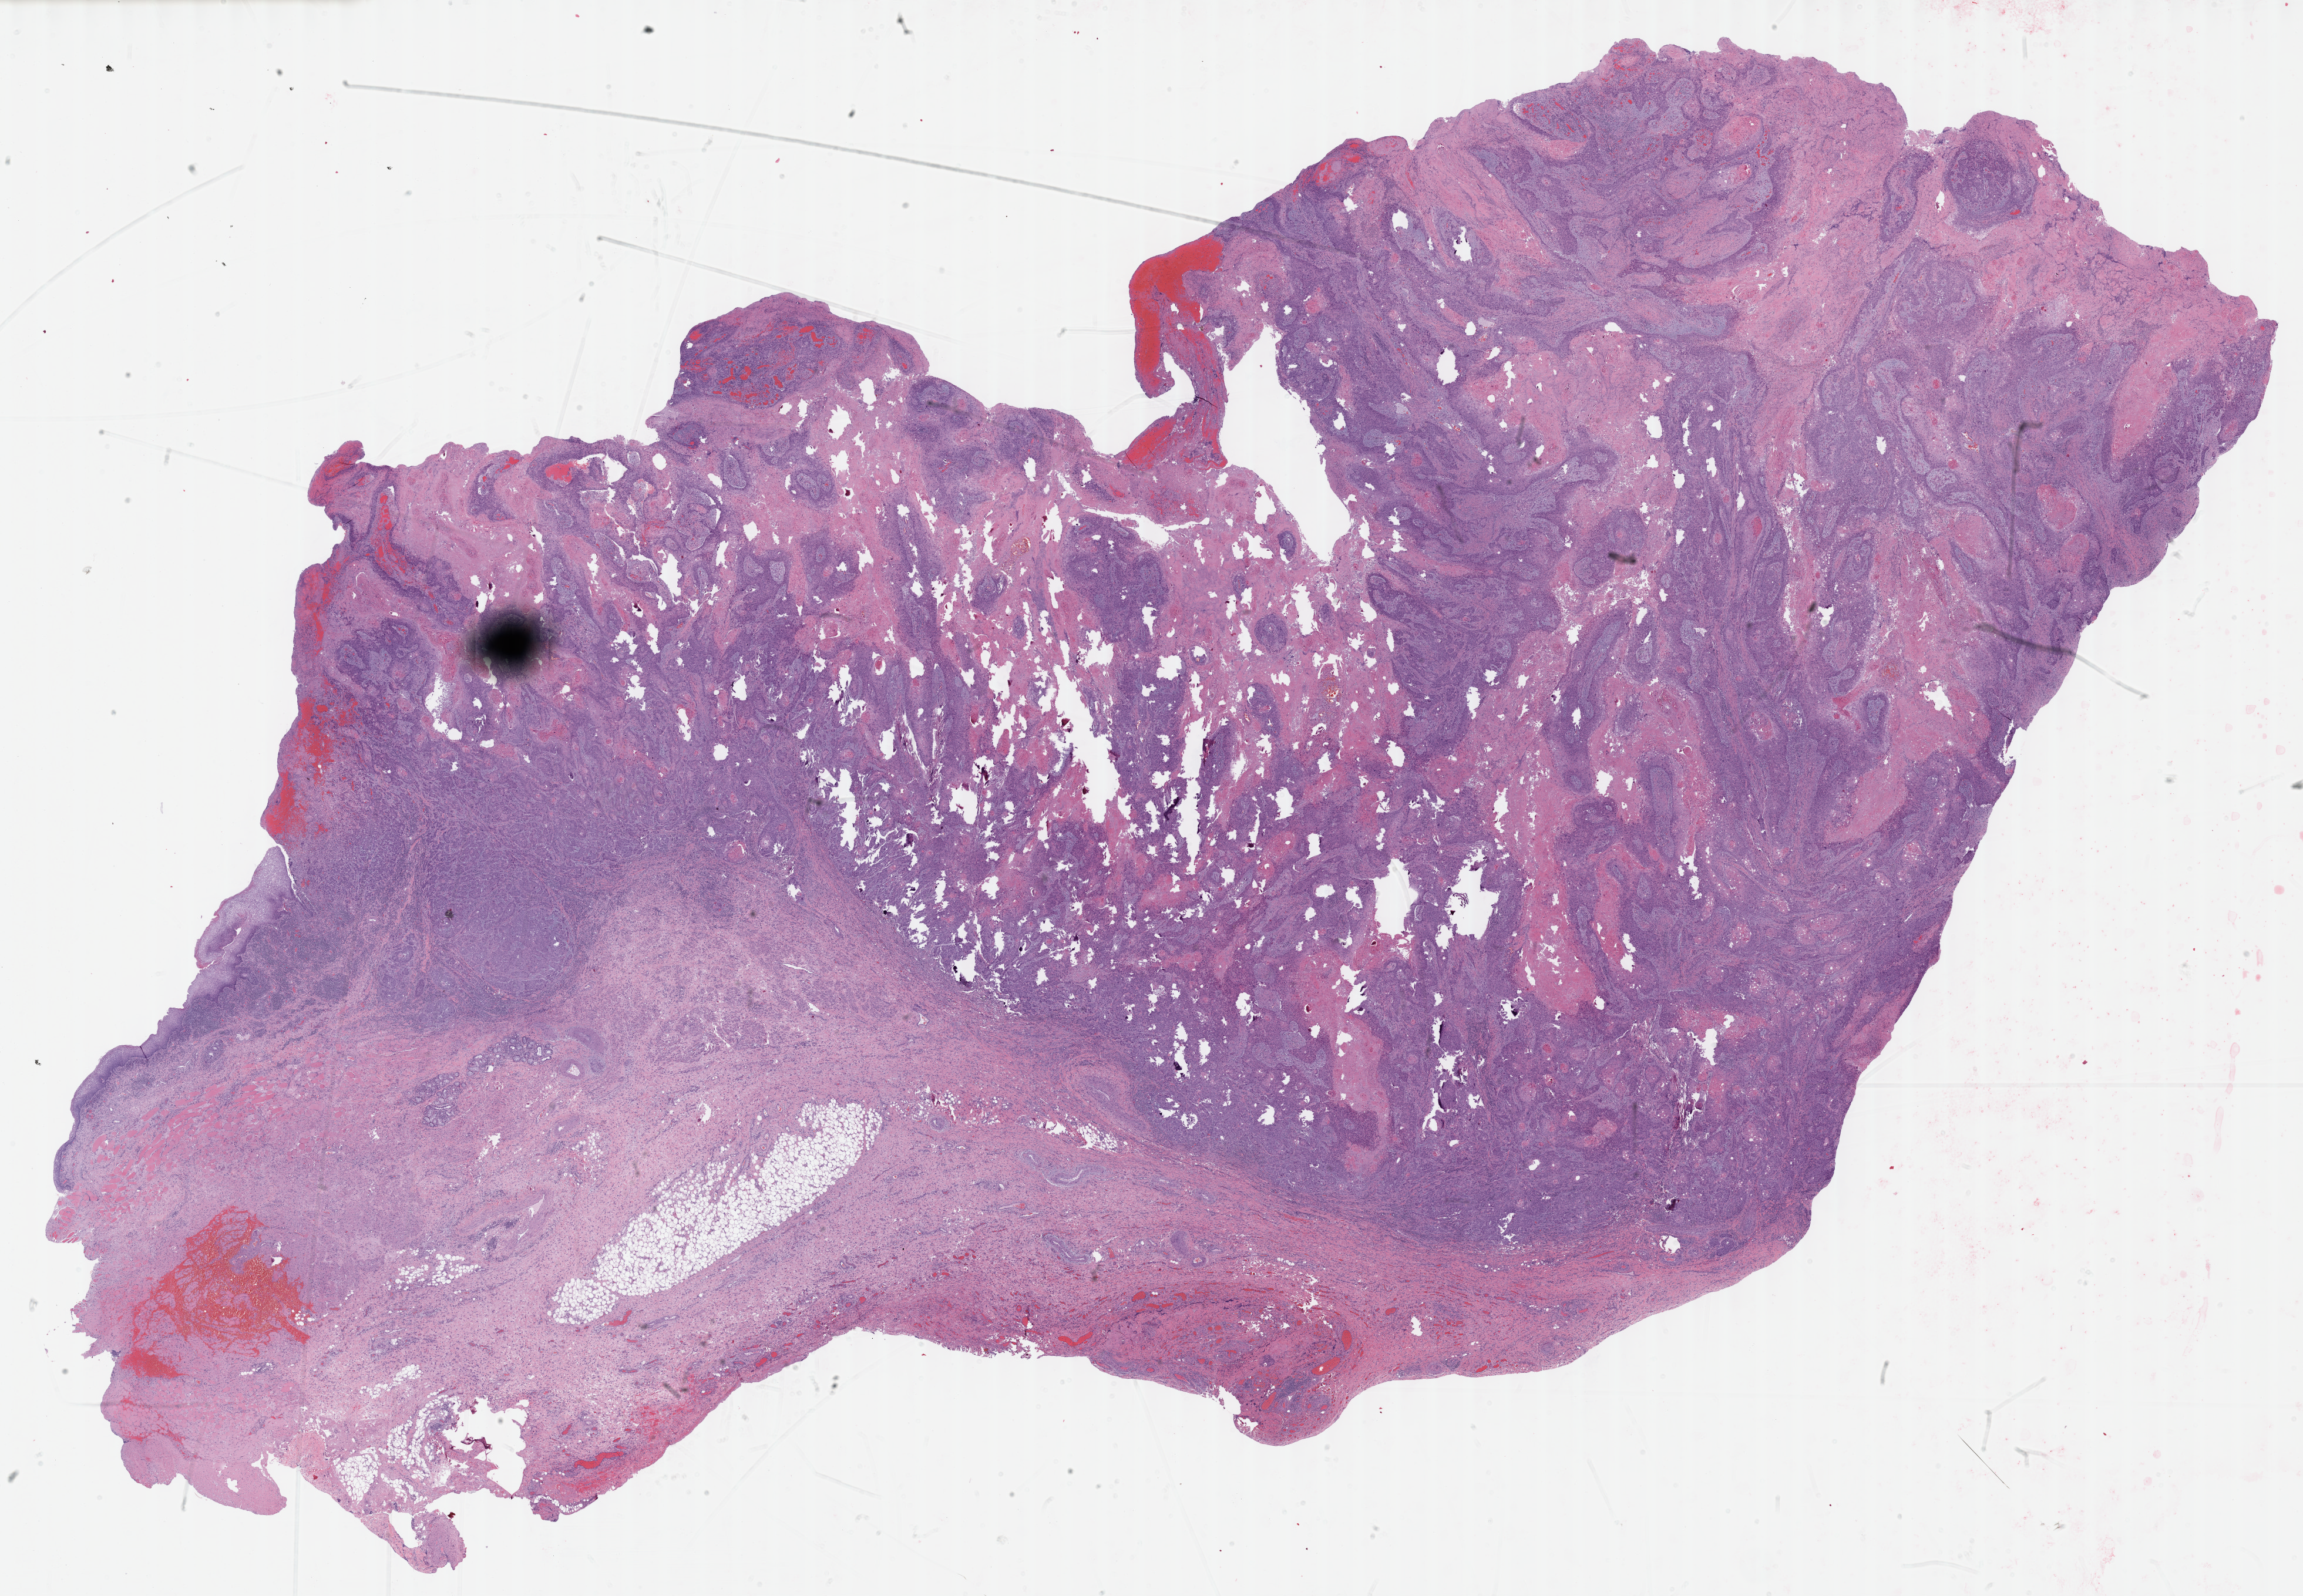
Whole-slide histology image, H&E, low-resolution overview of the scanned area, about 31.7 x 22.0 mm. Formalin-fixed paraffin-embedded (FFPE) diagnostic section. Head and neck, primary tumour sample. Male, age 85 years at initial diagnosis. Histologic grade: G2 (moderately differentiated).
Histologic diagnosis: Squamous cell carcinoma, NOS (larynx, NOS).